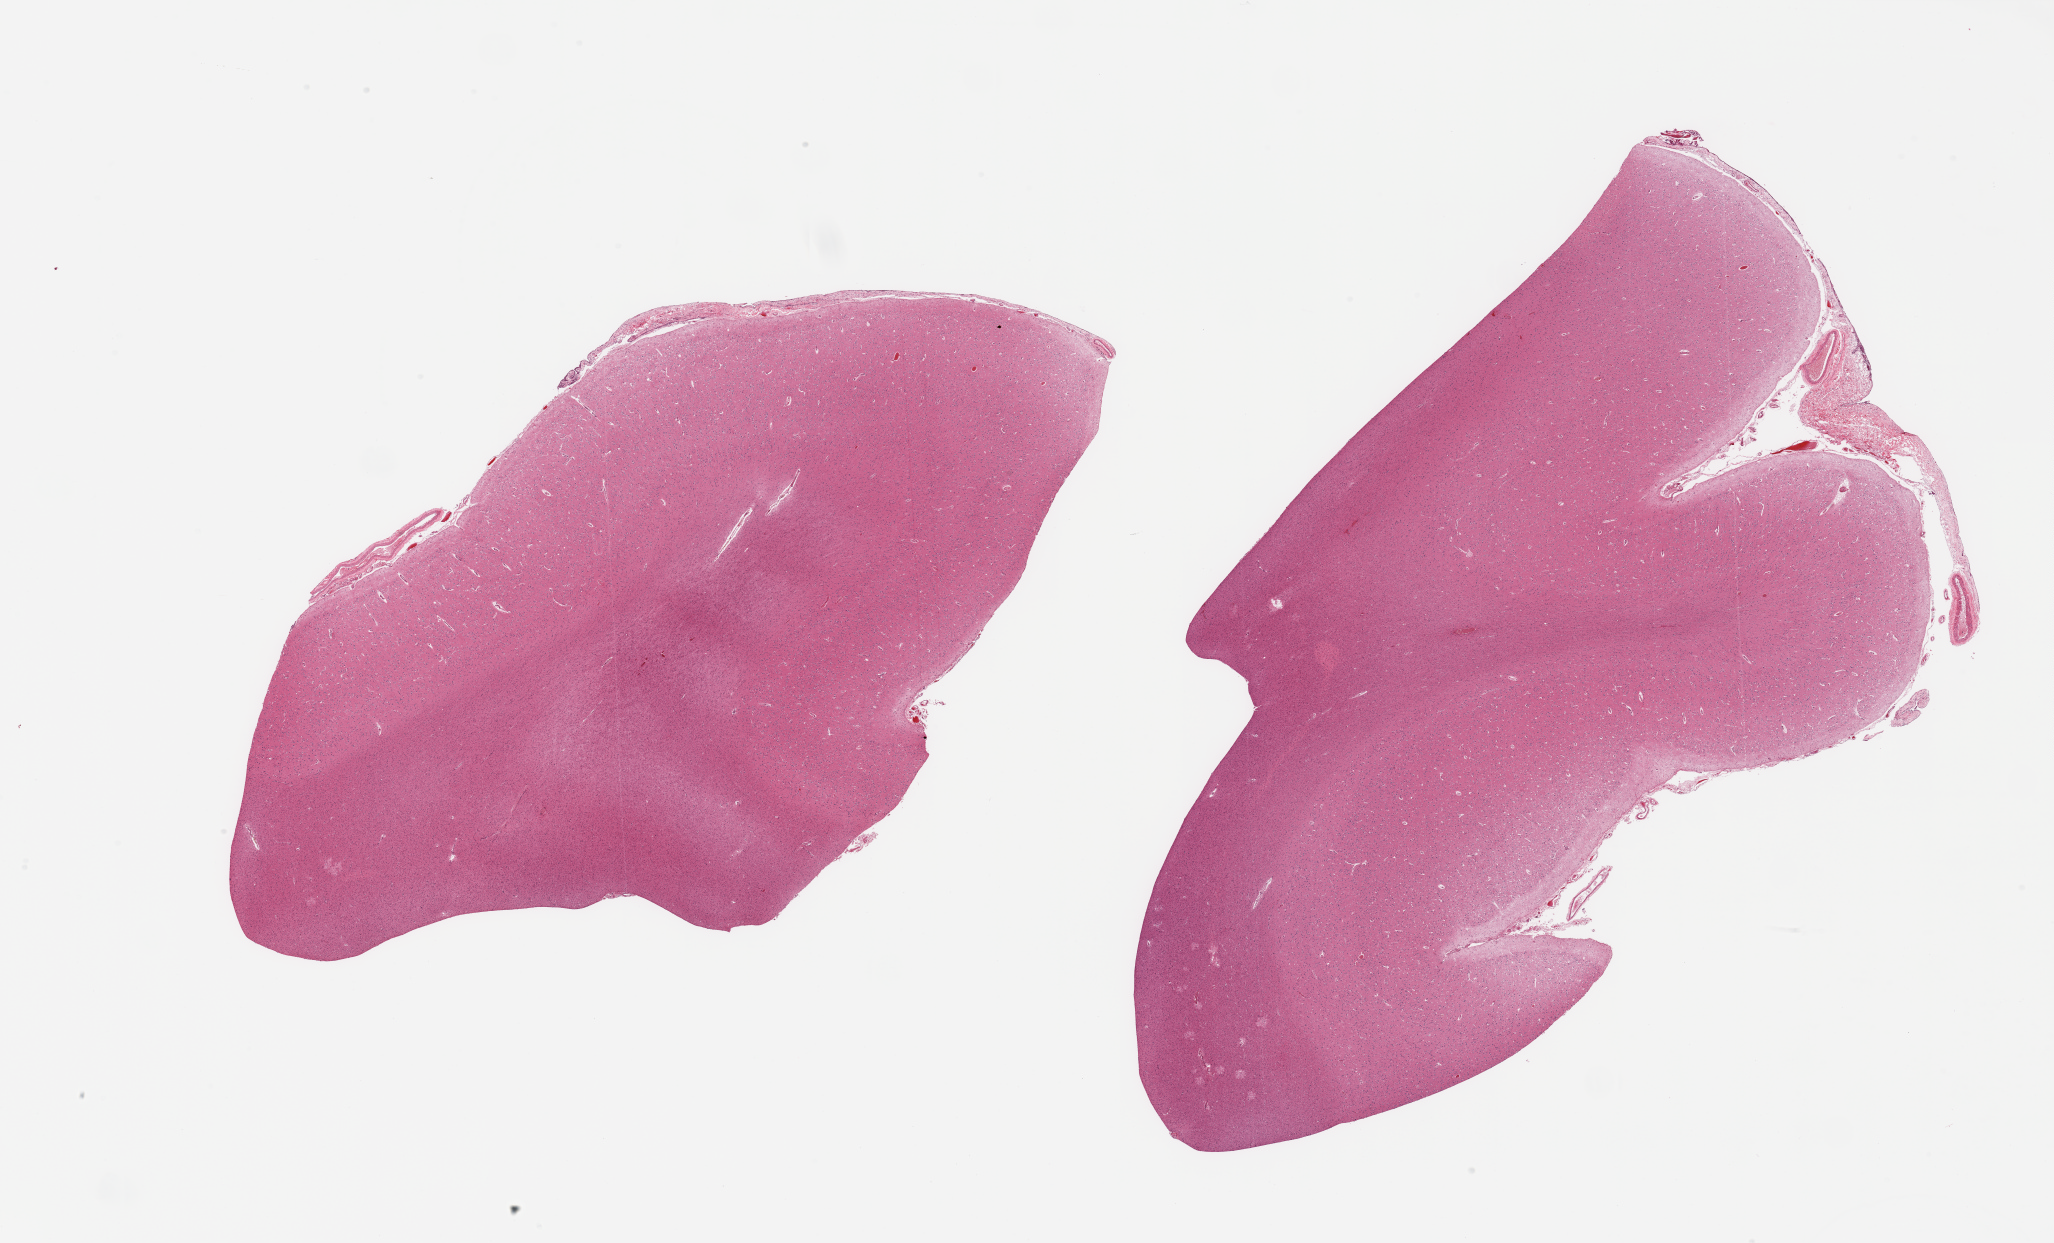
Whole-slide image, H&E stain — a low-resolution overview of the entire scanned area, about 32.5 x 19.7 mm; PAXgene-fixed, paraffin-embedded tissue; section of cerebral cortex (target tissue); tissue donor sample. Donor sex: male.
* review note (as recorded): 2 pieces; meninges attached